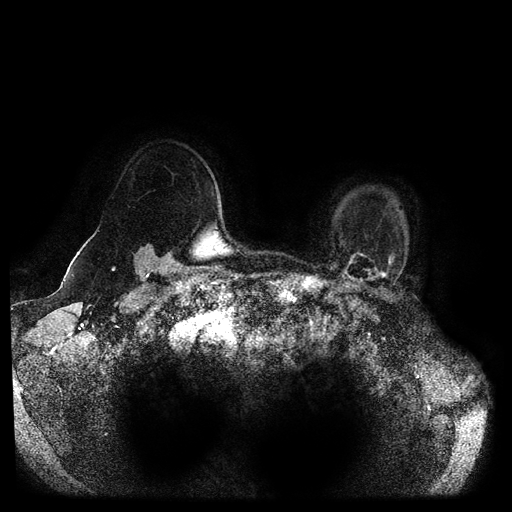
Breast MRI (dynamic contrast-enhanced, multi-phase), one axial slice; slice 86 of 116 in the series (ordered by position); dynamic contrast-enhanced series, time point 2 of 5 at this slice position (early post-contrast); 1.5 T; TE 2.6 ms, TR 5.3 ms; 512 × 512 image matrix, field of view 370 × 370 mm. Female patient, age 55 years.
Structures marked on this image (semi-automatically segmented with operator editing):
- breast lesion (labelled benign in the annotation): box from (x=342, y=252) to (x=395, y=285) px